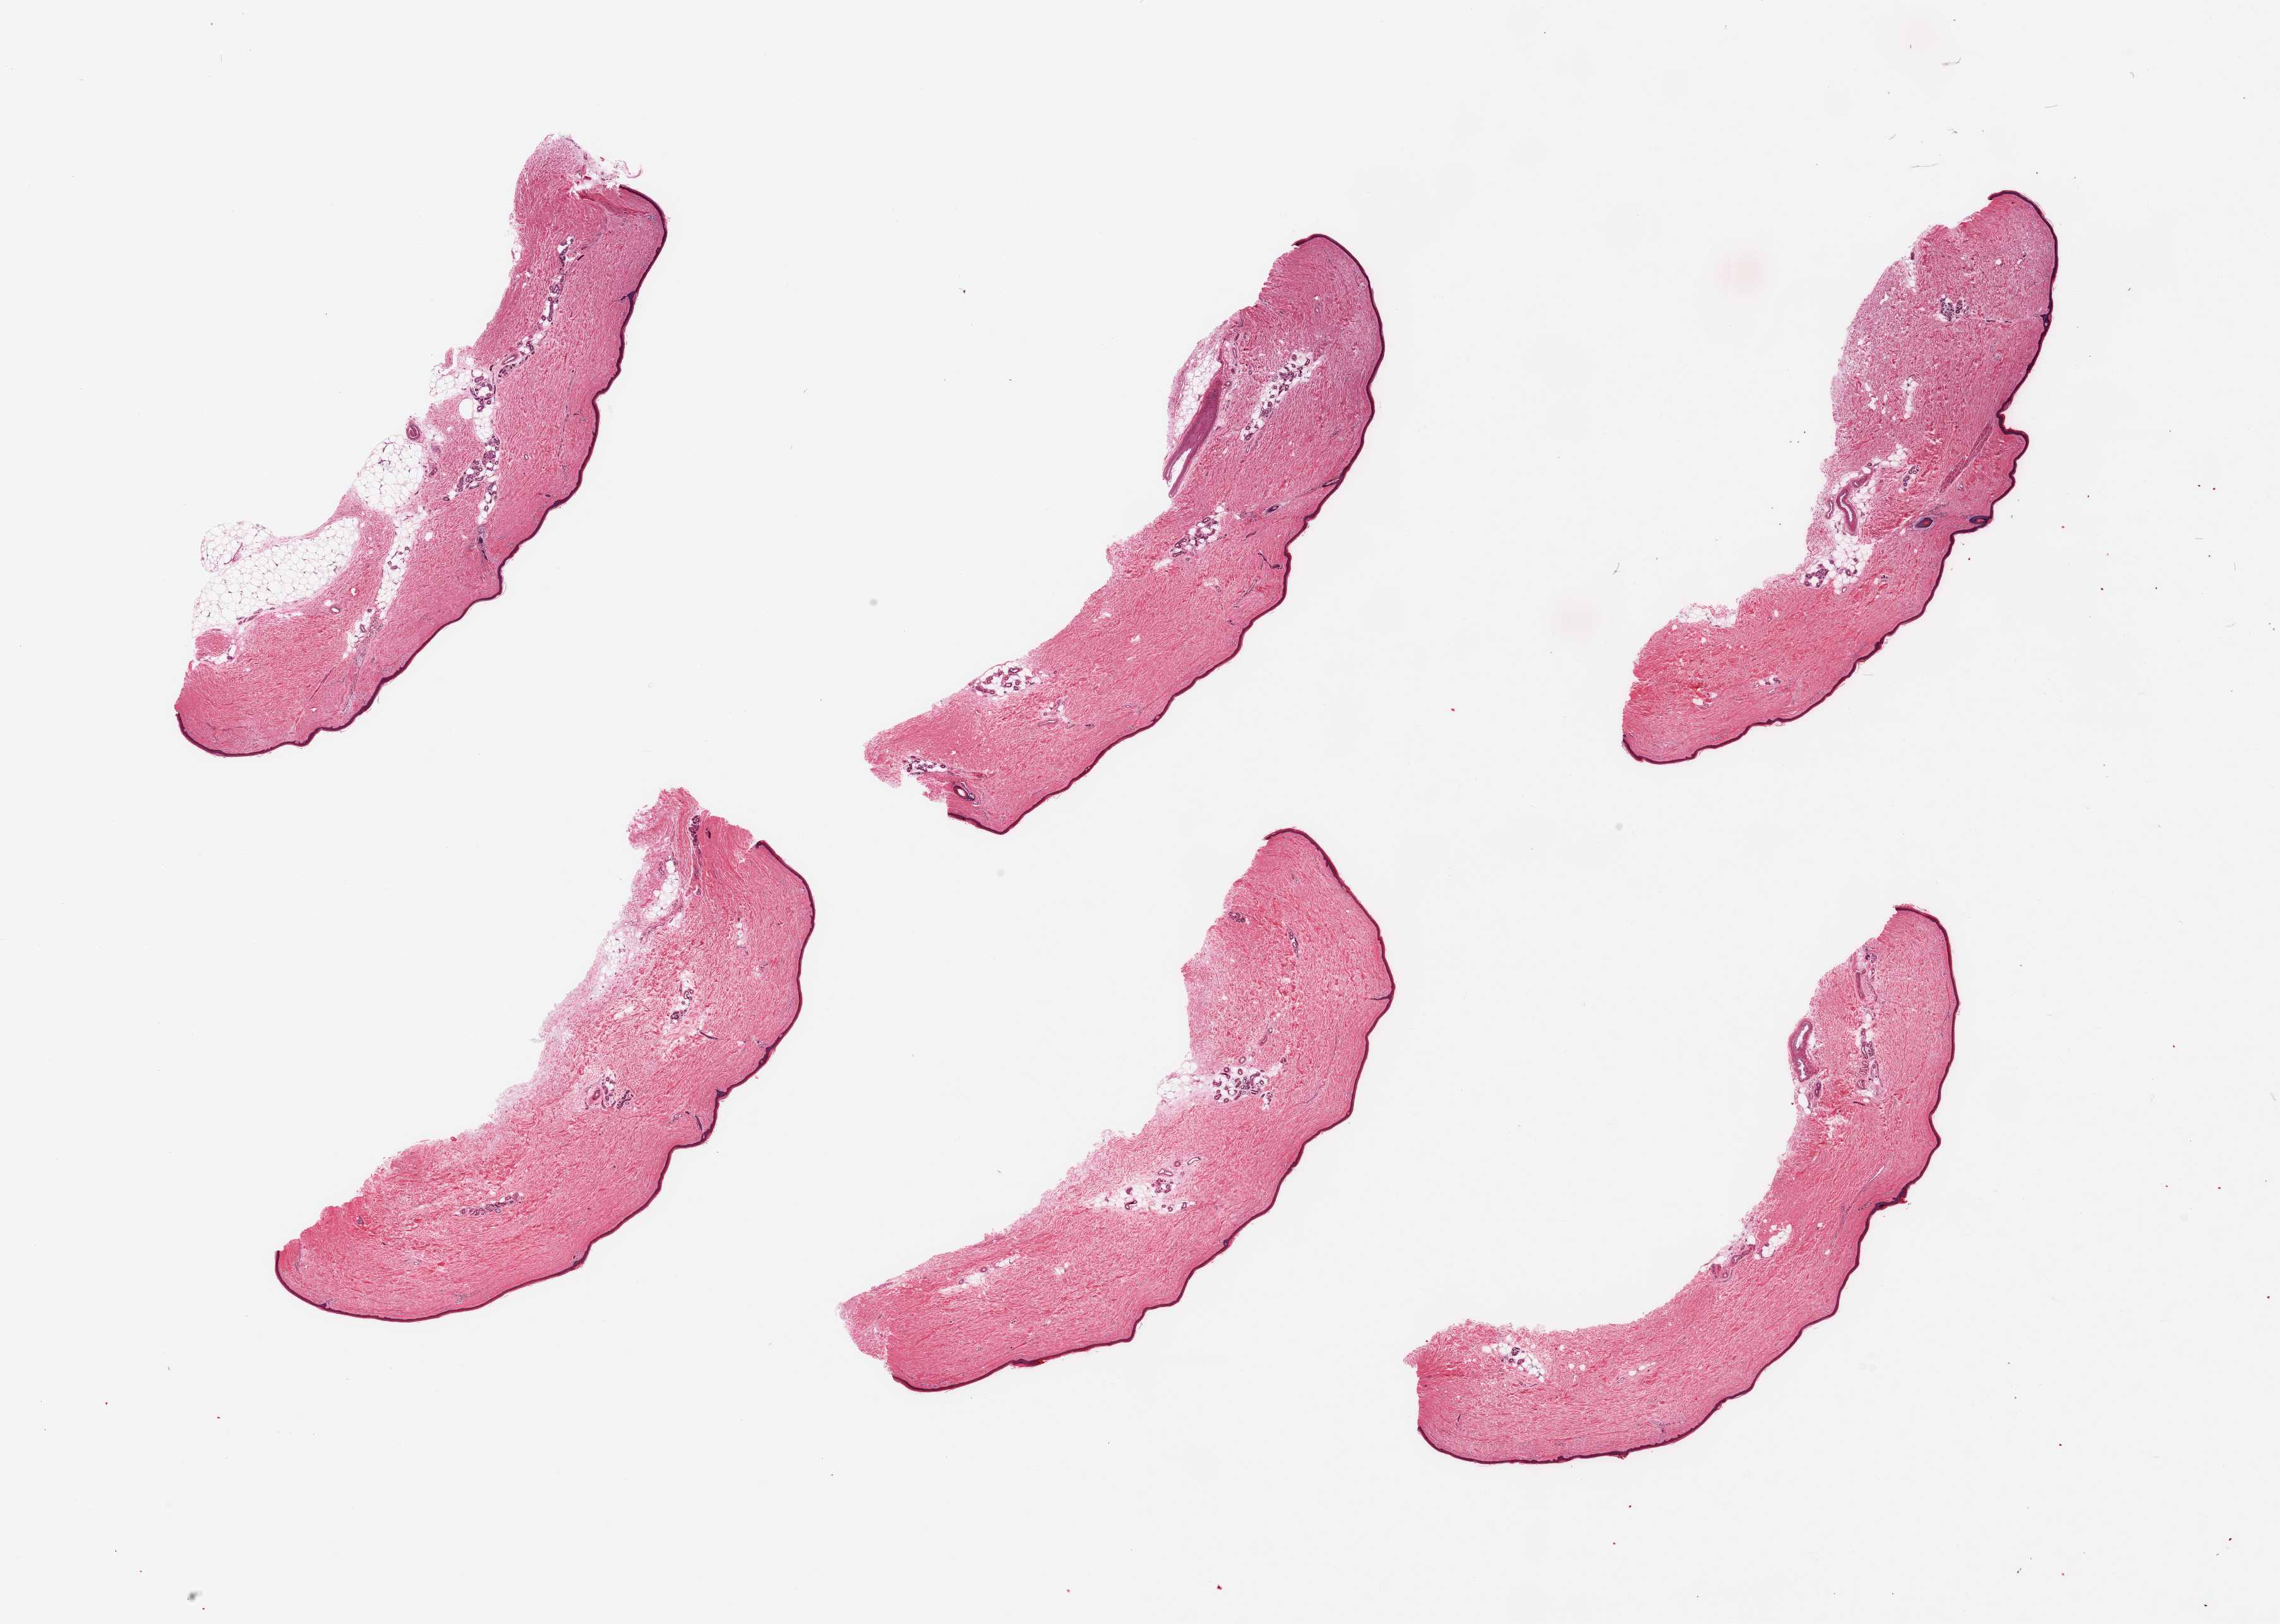
Digitized H&E-stained section, brightfield — a low-resolution overview of the entire scanned area, about 28.5 x 20.3 mm (slide scanned at 20x). PAXgene-fixed paraffin-embedded (PFPE) section. Sampled site (target tissue): skin of lower leg. Tissue donor sample. Female donor.
- review note (as recorded): 6 pieces; well trimmed; 10% dermal fat; 28um thick epidermis